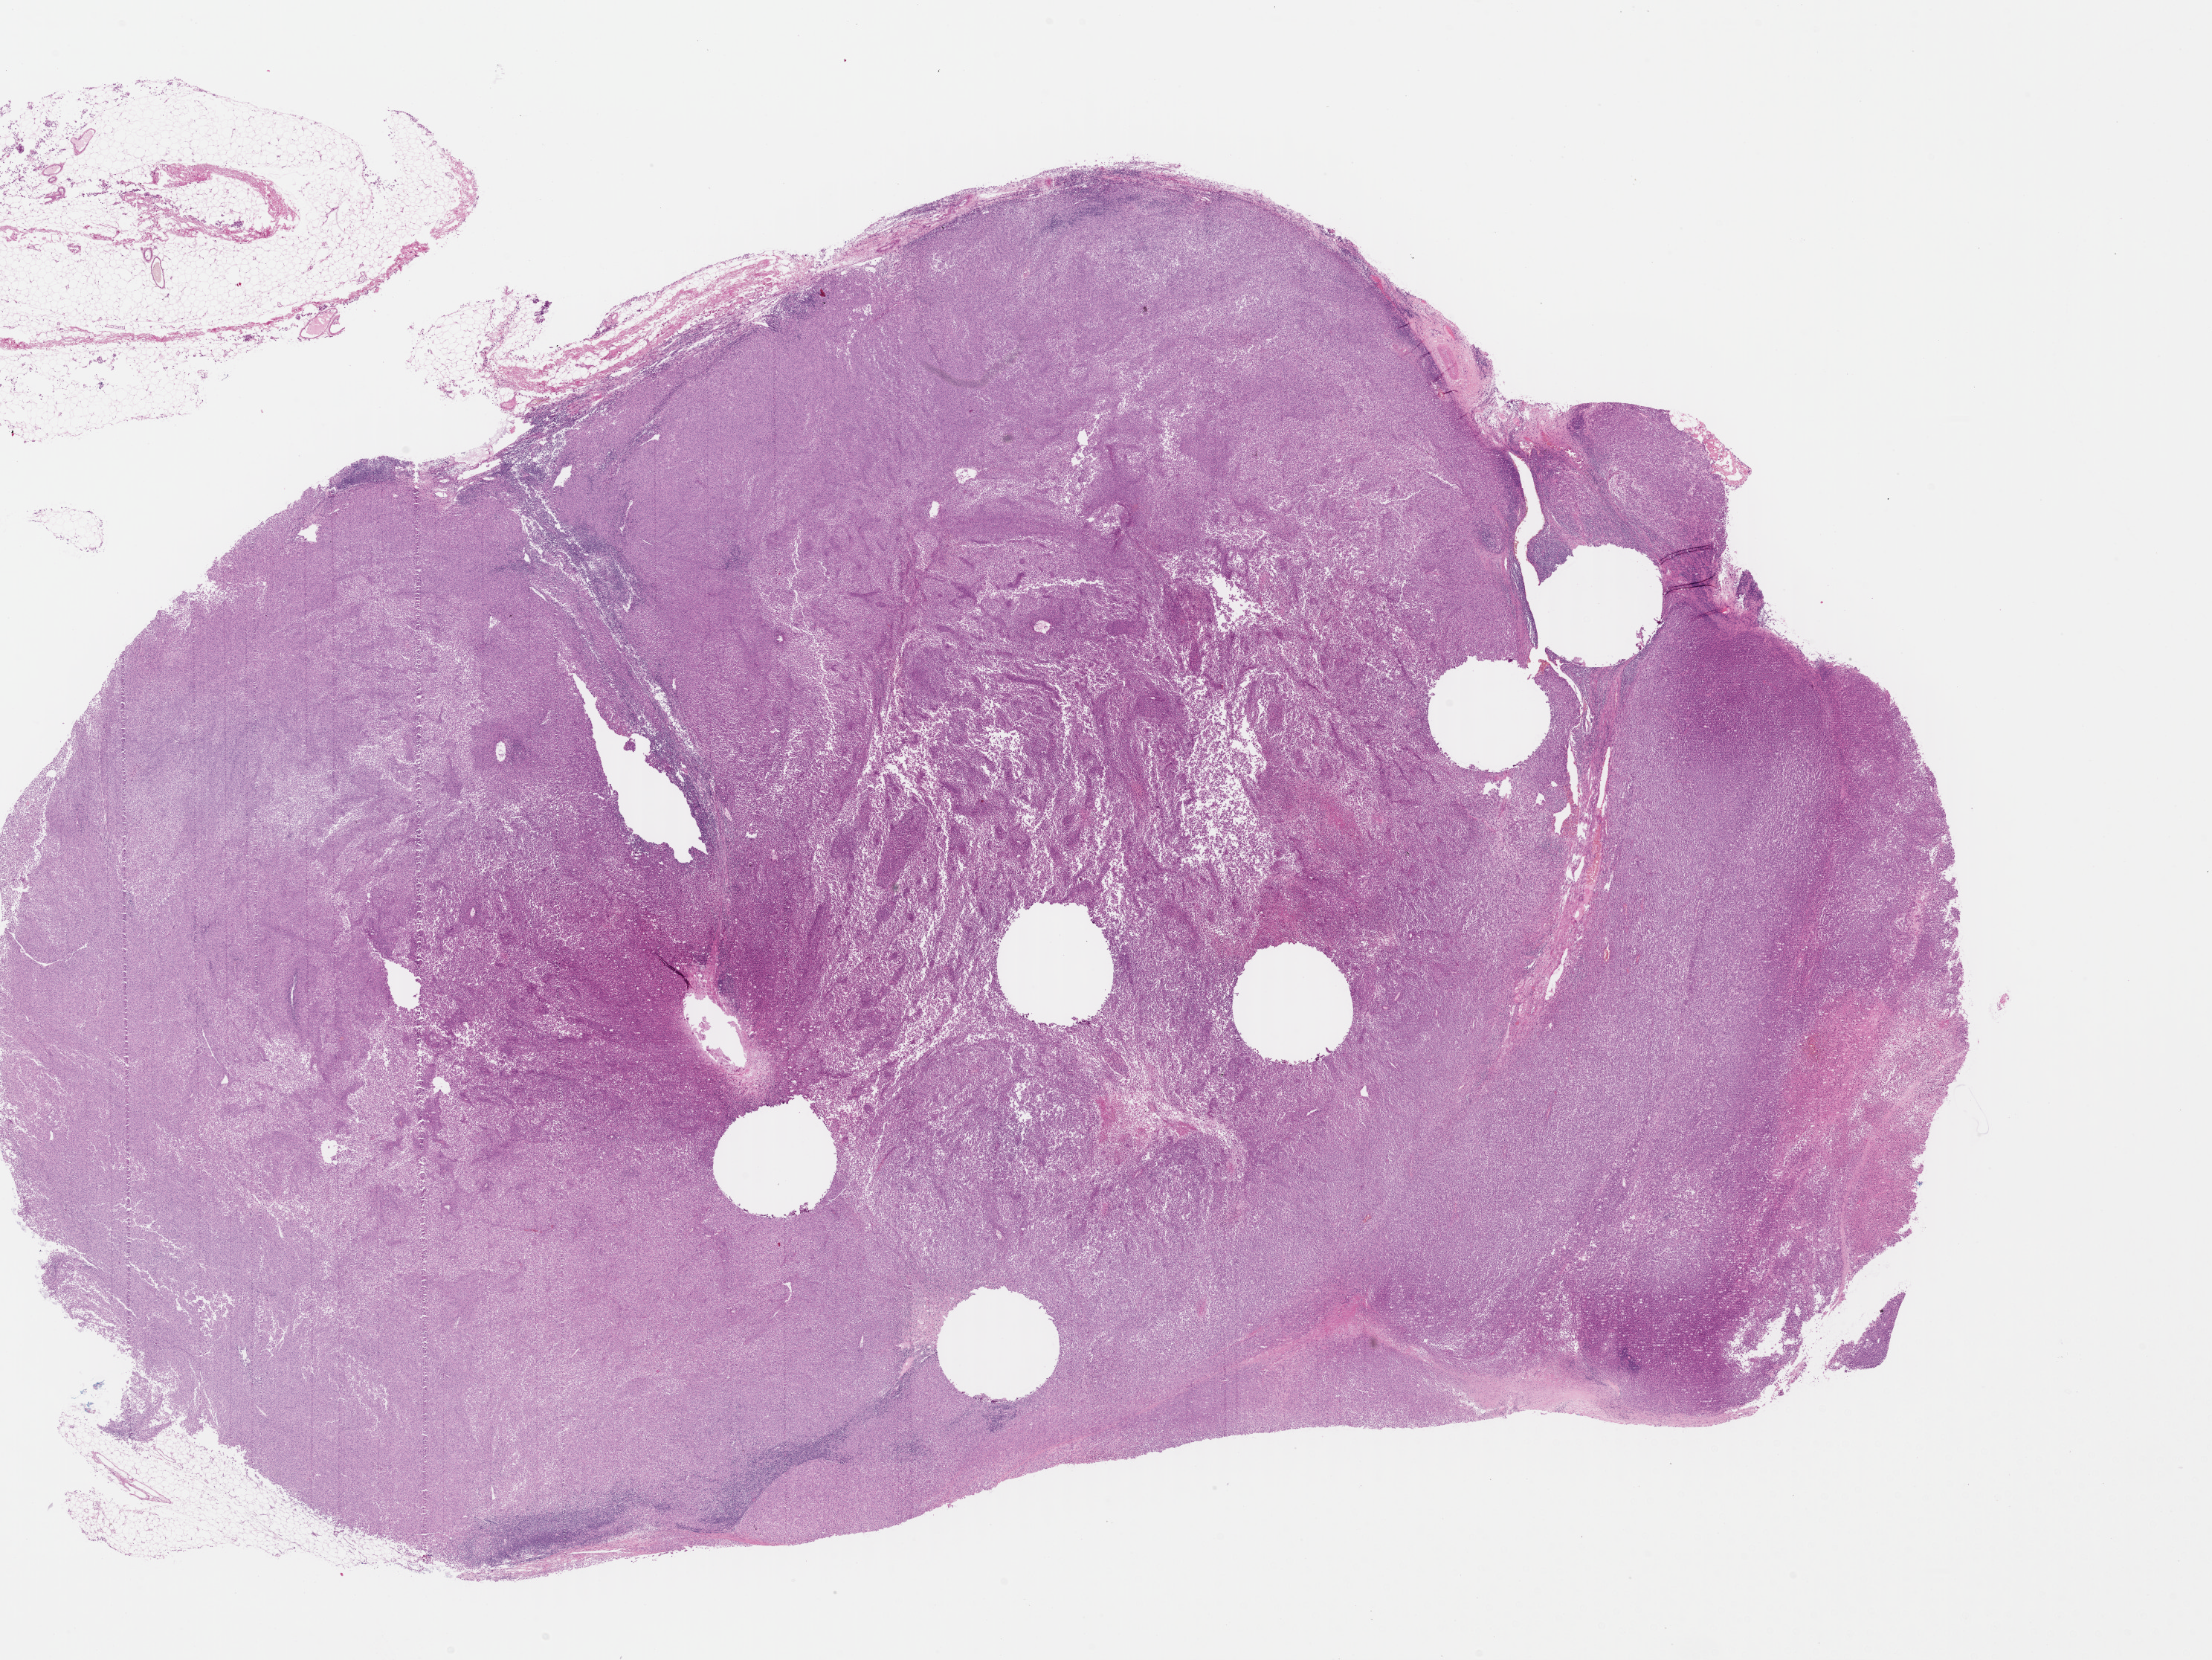
Digitized H&E tissue section (whole slide), whole scanned area (about 23.4 x 17.5 mm, from a 40x scan) shown as a low-resolution overview; formalin-fixed paraffin-embedded (FFPE) diagnostic section; sample: primary tumour, skin. Female patient; age at initial diagnosis 39 years.
Diagnosis: Malignant melanoma, NOS.